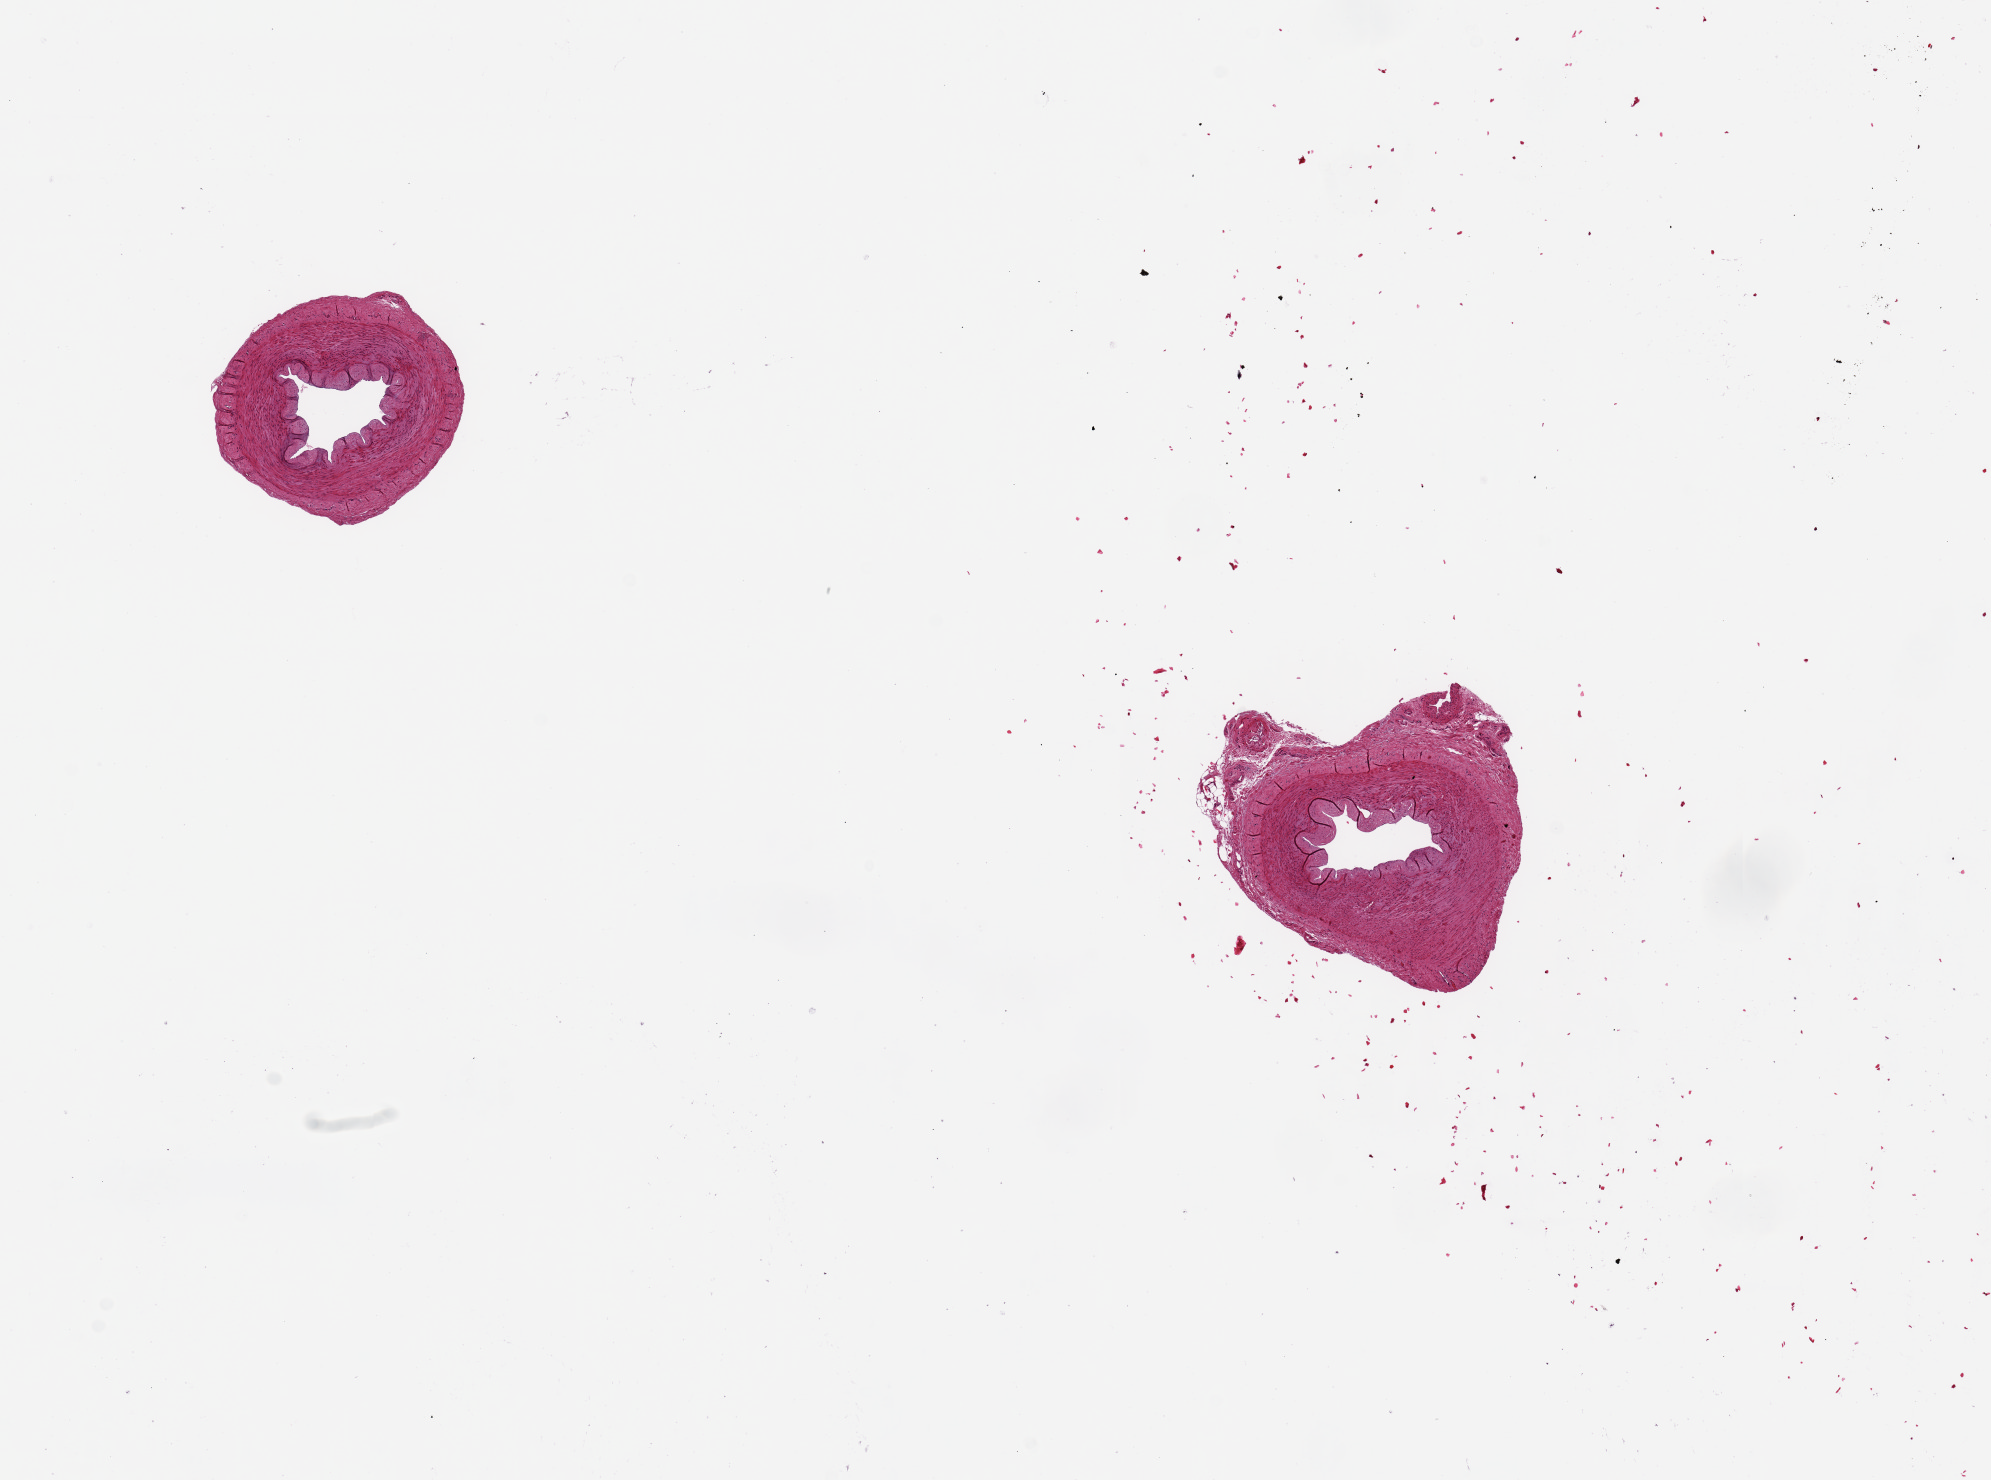
Haematoxylin and eosin whole-slide image — whole scanned area (about 15.8 x 11.7 mm) shown as a low-resolution overview. PAXgene-fixed, paraffin-embedded tissue. Target tissue: tibial artery. Donor tissue sample. Donor sex: male.
Pathologist's review note for this sample: 2 pieces ~2mm d. Good clean specimens.